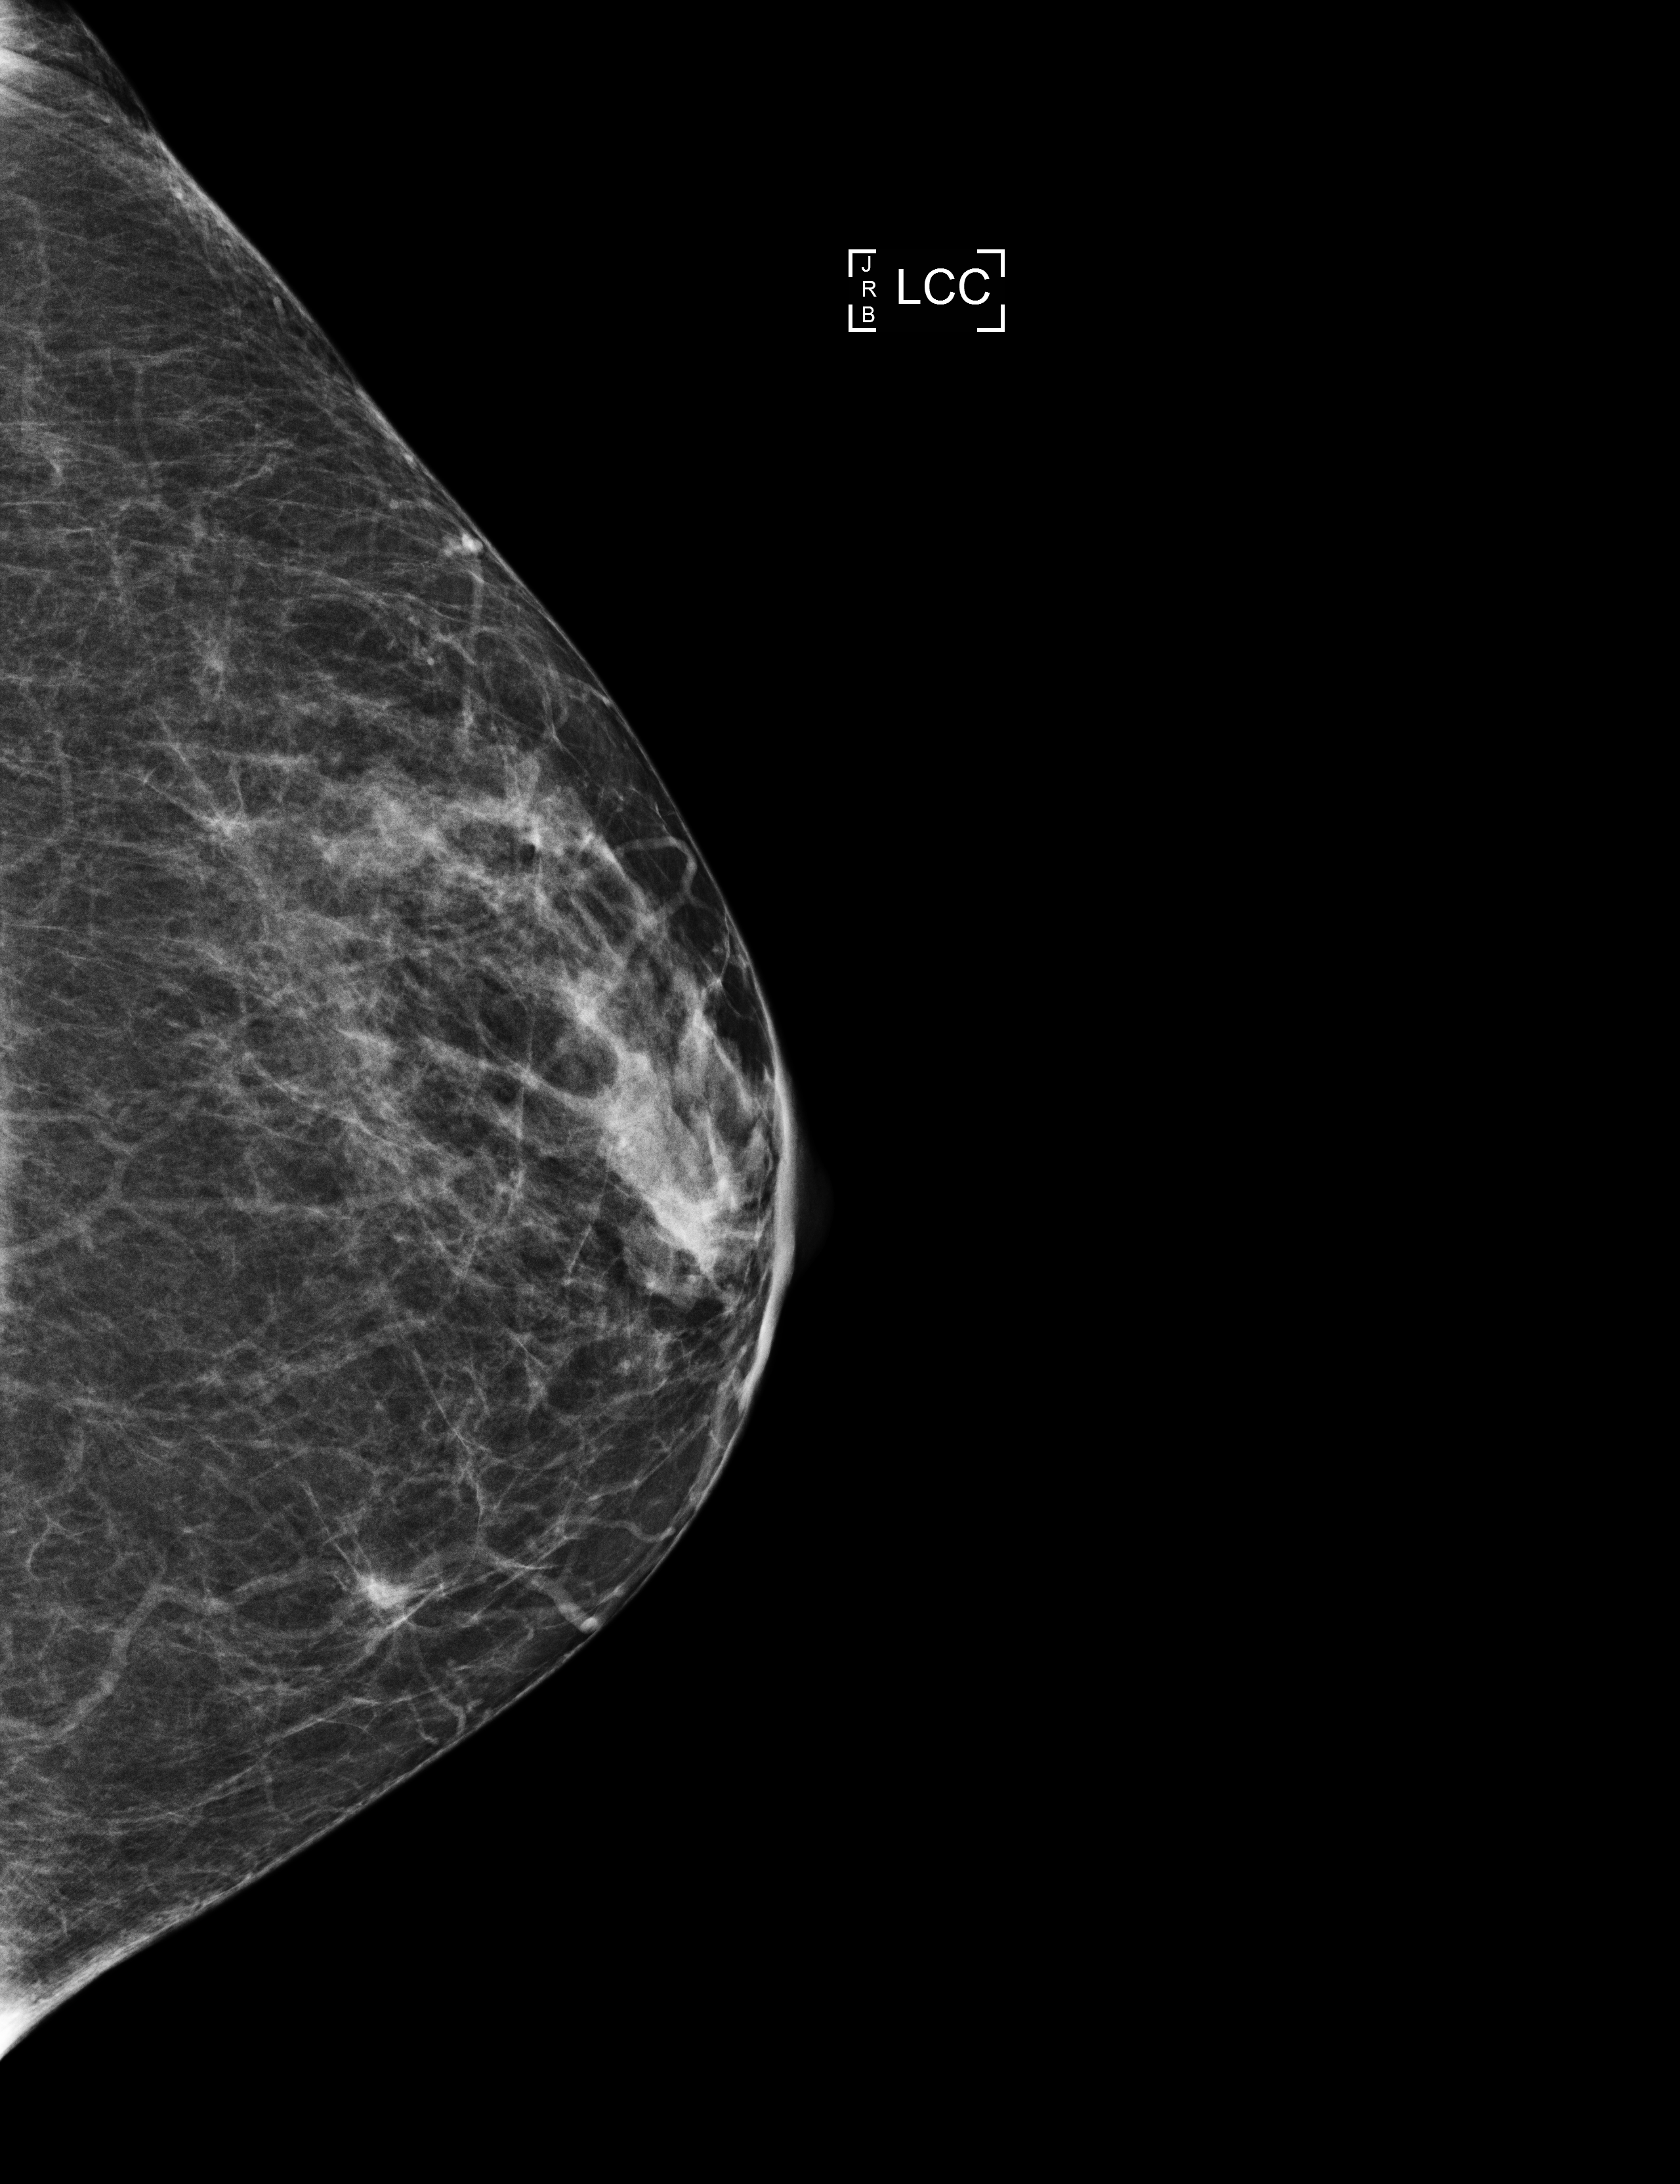
Screening examination, compressed breast thickness 41 mm, system: Selenia Dimensions. Patient: female, 60 years.
Image type: full-field digital mammogram. Breast: left. Projection: CC view.